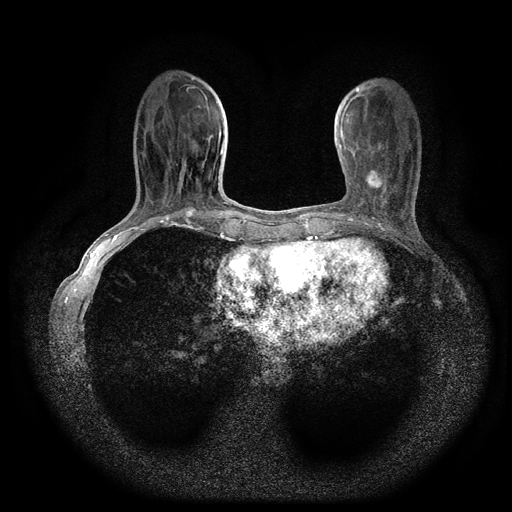
Breast MRI (dynamic contrast-enhanced, multi-phase), one axial slice; slice 33 of 116 in the series (ordered by position); dynamic contrast-enhanced series, time point 2 of 5 at this slice position (early post-contrast); 1.5 T; TE 2.7 ms, TR 5.4 ms; 2 mm slice thickness; 512 × 512 image matrix, field of view 330 × 330 mm. Patient: female, 49 years.
Annotated regions visible in this slice (semi-automatically segmented with operator editing):
- breast lesion (labelled 'tumour' in the annotation; benign lesions carry a separate 'benign' label): bounding box <362,169,385,192> (left, top, right, bottom; pixels)